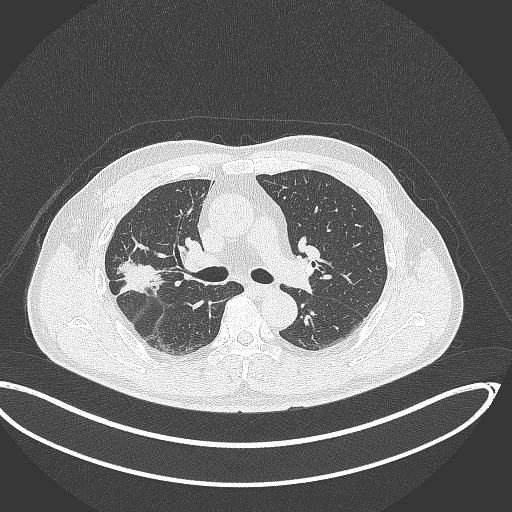
Chest CT, one axial slice; slice 209 of 391 in the series (ordered by position); 120 kVp; lung window (W 1500 / L -600 HU); 1 mm slice thickness; 512 × 512 image matrix. Patient: male, 63 years. From the clinical record (not read from this slice): clinical TNM (as recorded): T1c N0 M0; histopathological grade: G2-3.
Annotated regions visible in this slice (rectangle marked by the reading radiologist):
- lung tumour (recorded histology: adenocarcinoma): bounding box [x1, y1, x2, y2] px = [112, 251, 169, 303]